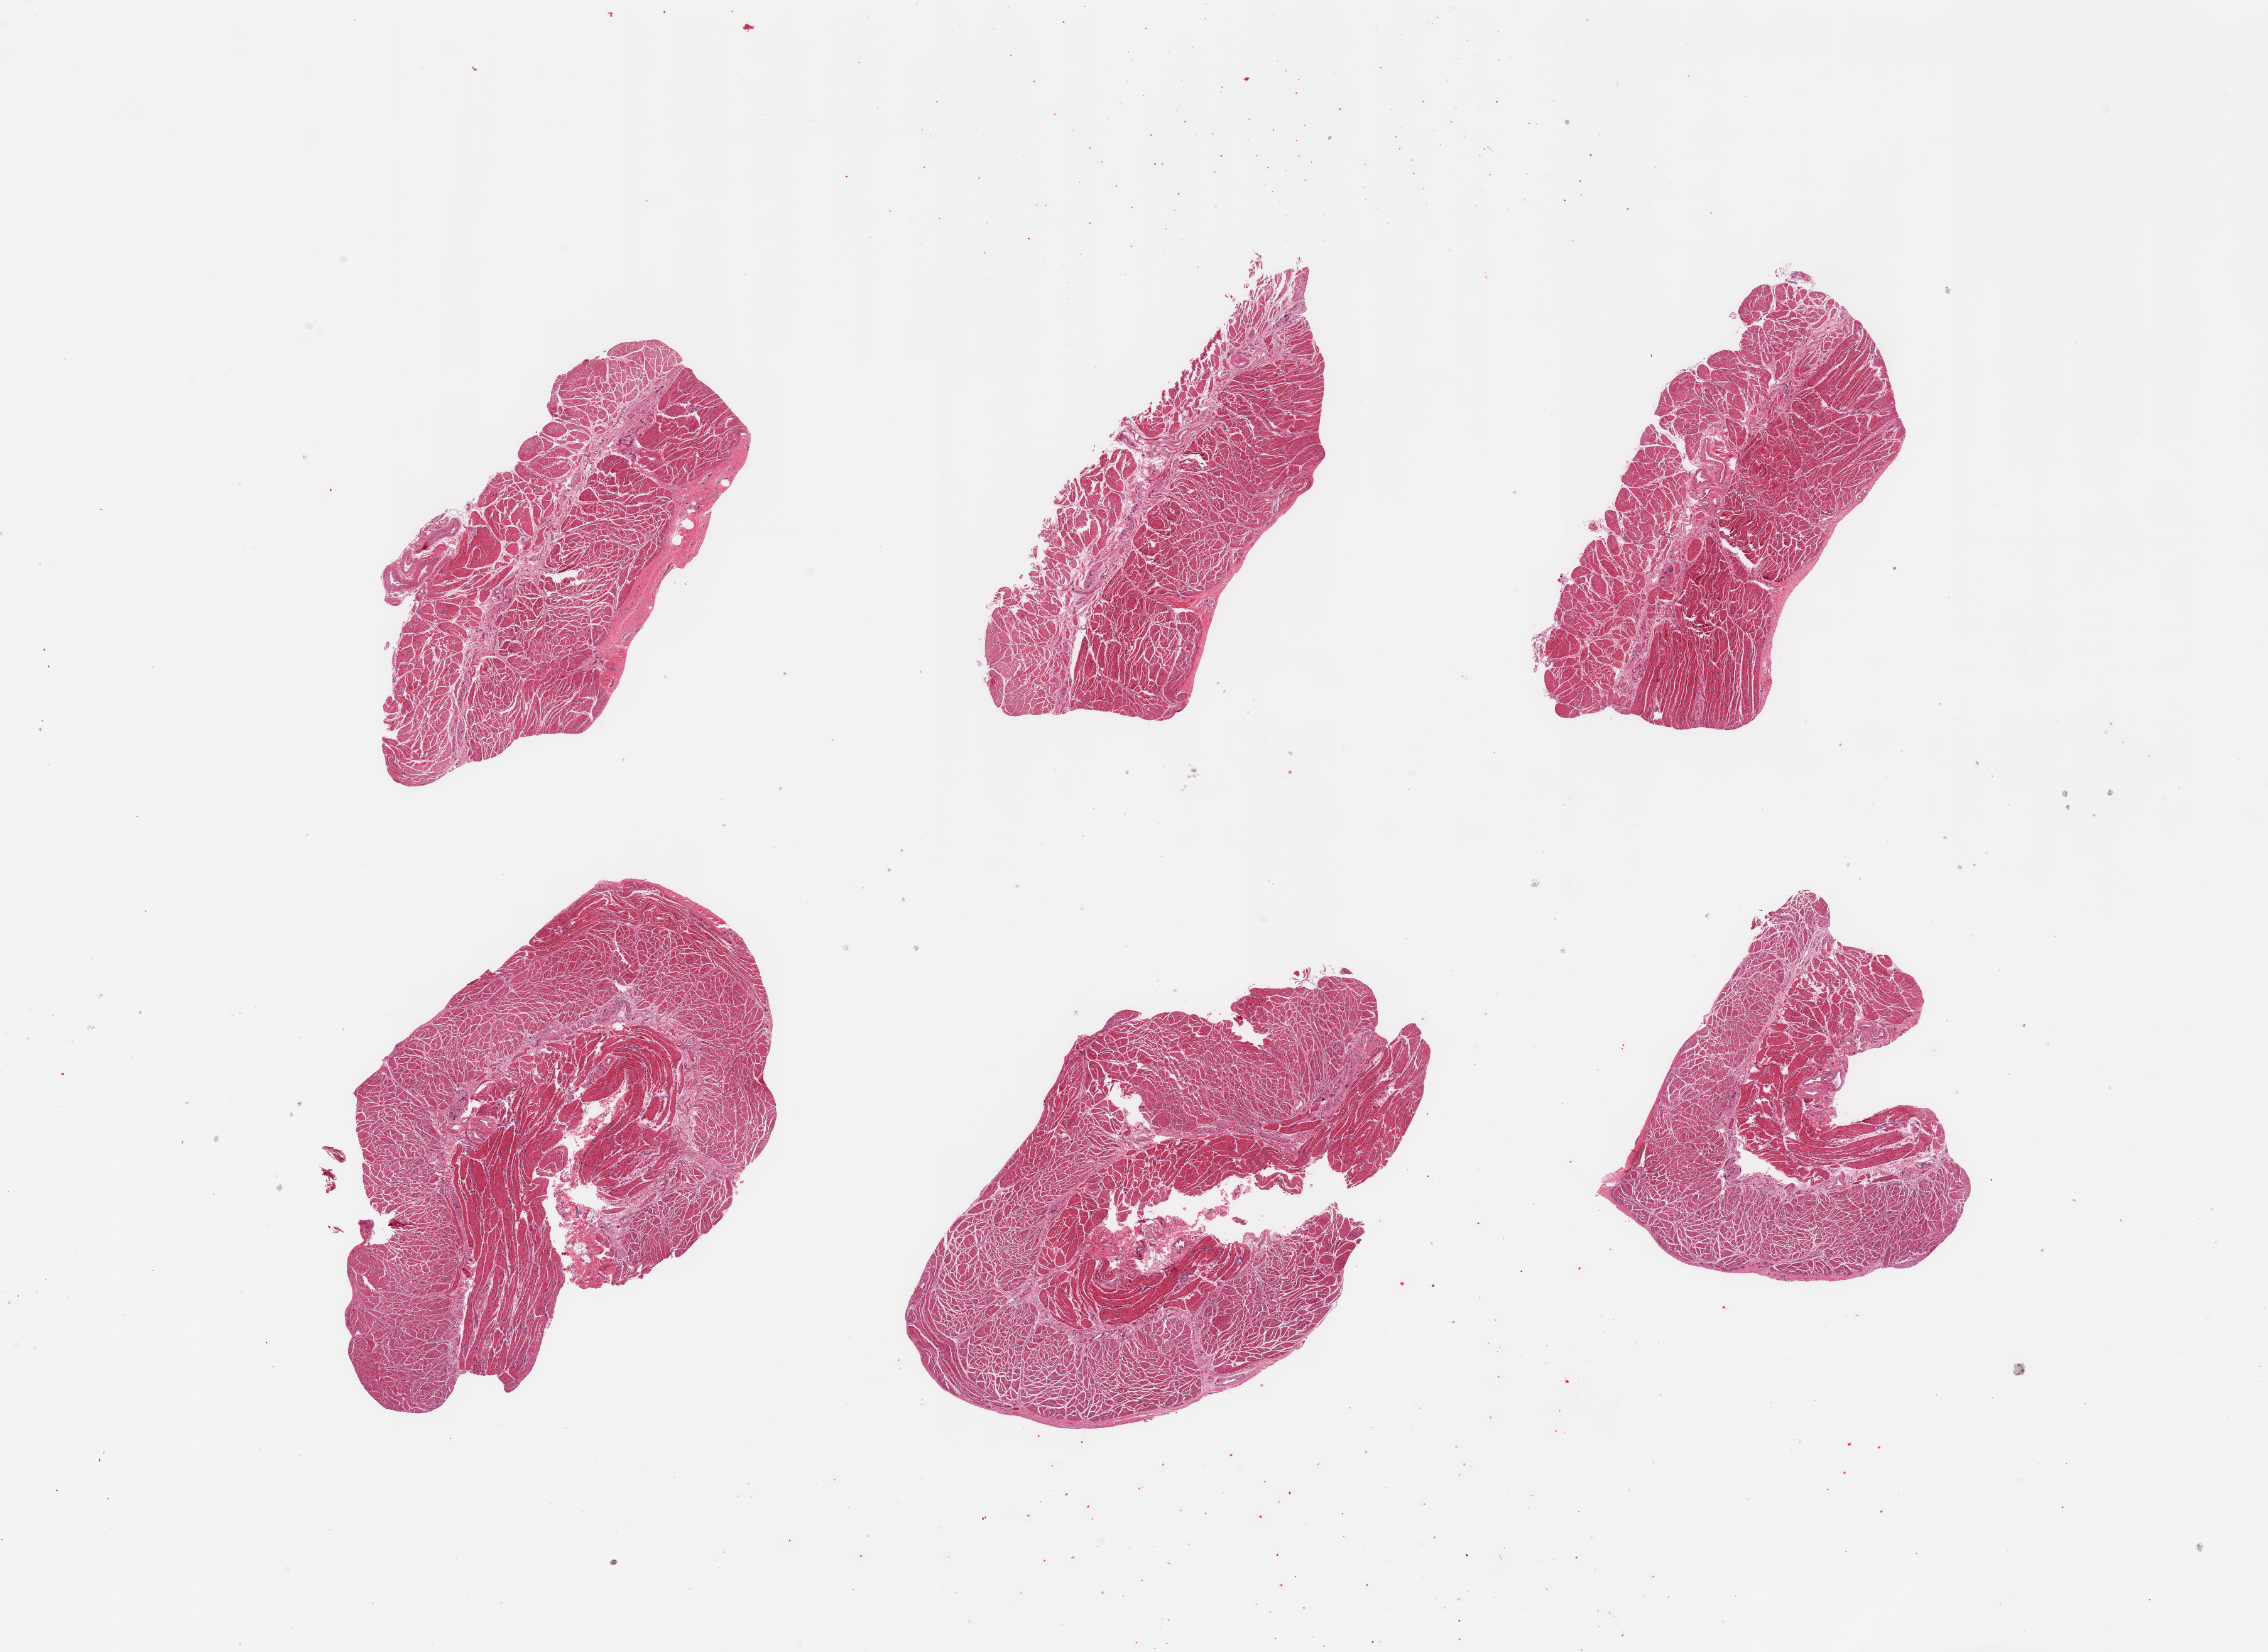
Haematoxylin and eosin whole-slide image, a low-resolution overview of the entire scanned area, about 28.5 x 20.8 mm (acquisition: 20x scan); PAXgene-fixed paraffin-embedded (PFPE) section; section of esophageal muscle (target tissue); tissue donor sample. Male donor.
Pathologist's review note for this sample: 6 pieces; well trimmed muscle.